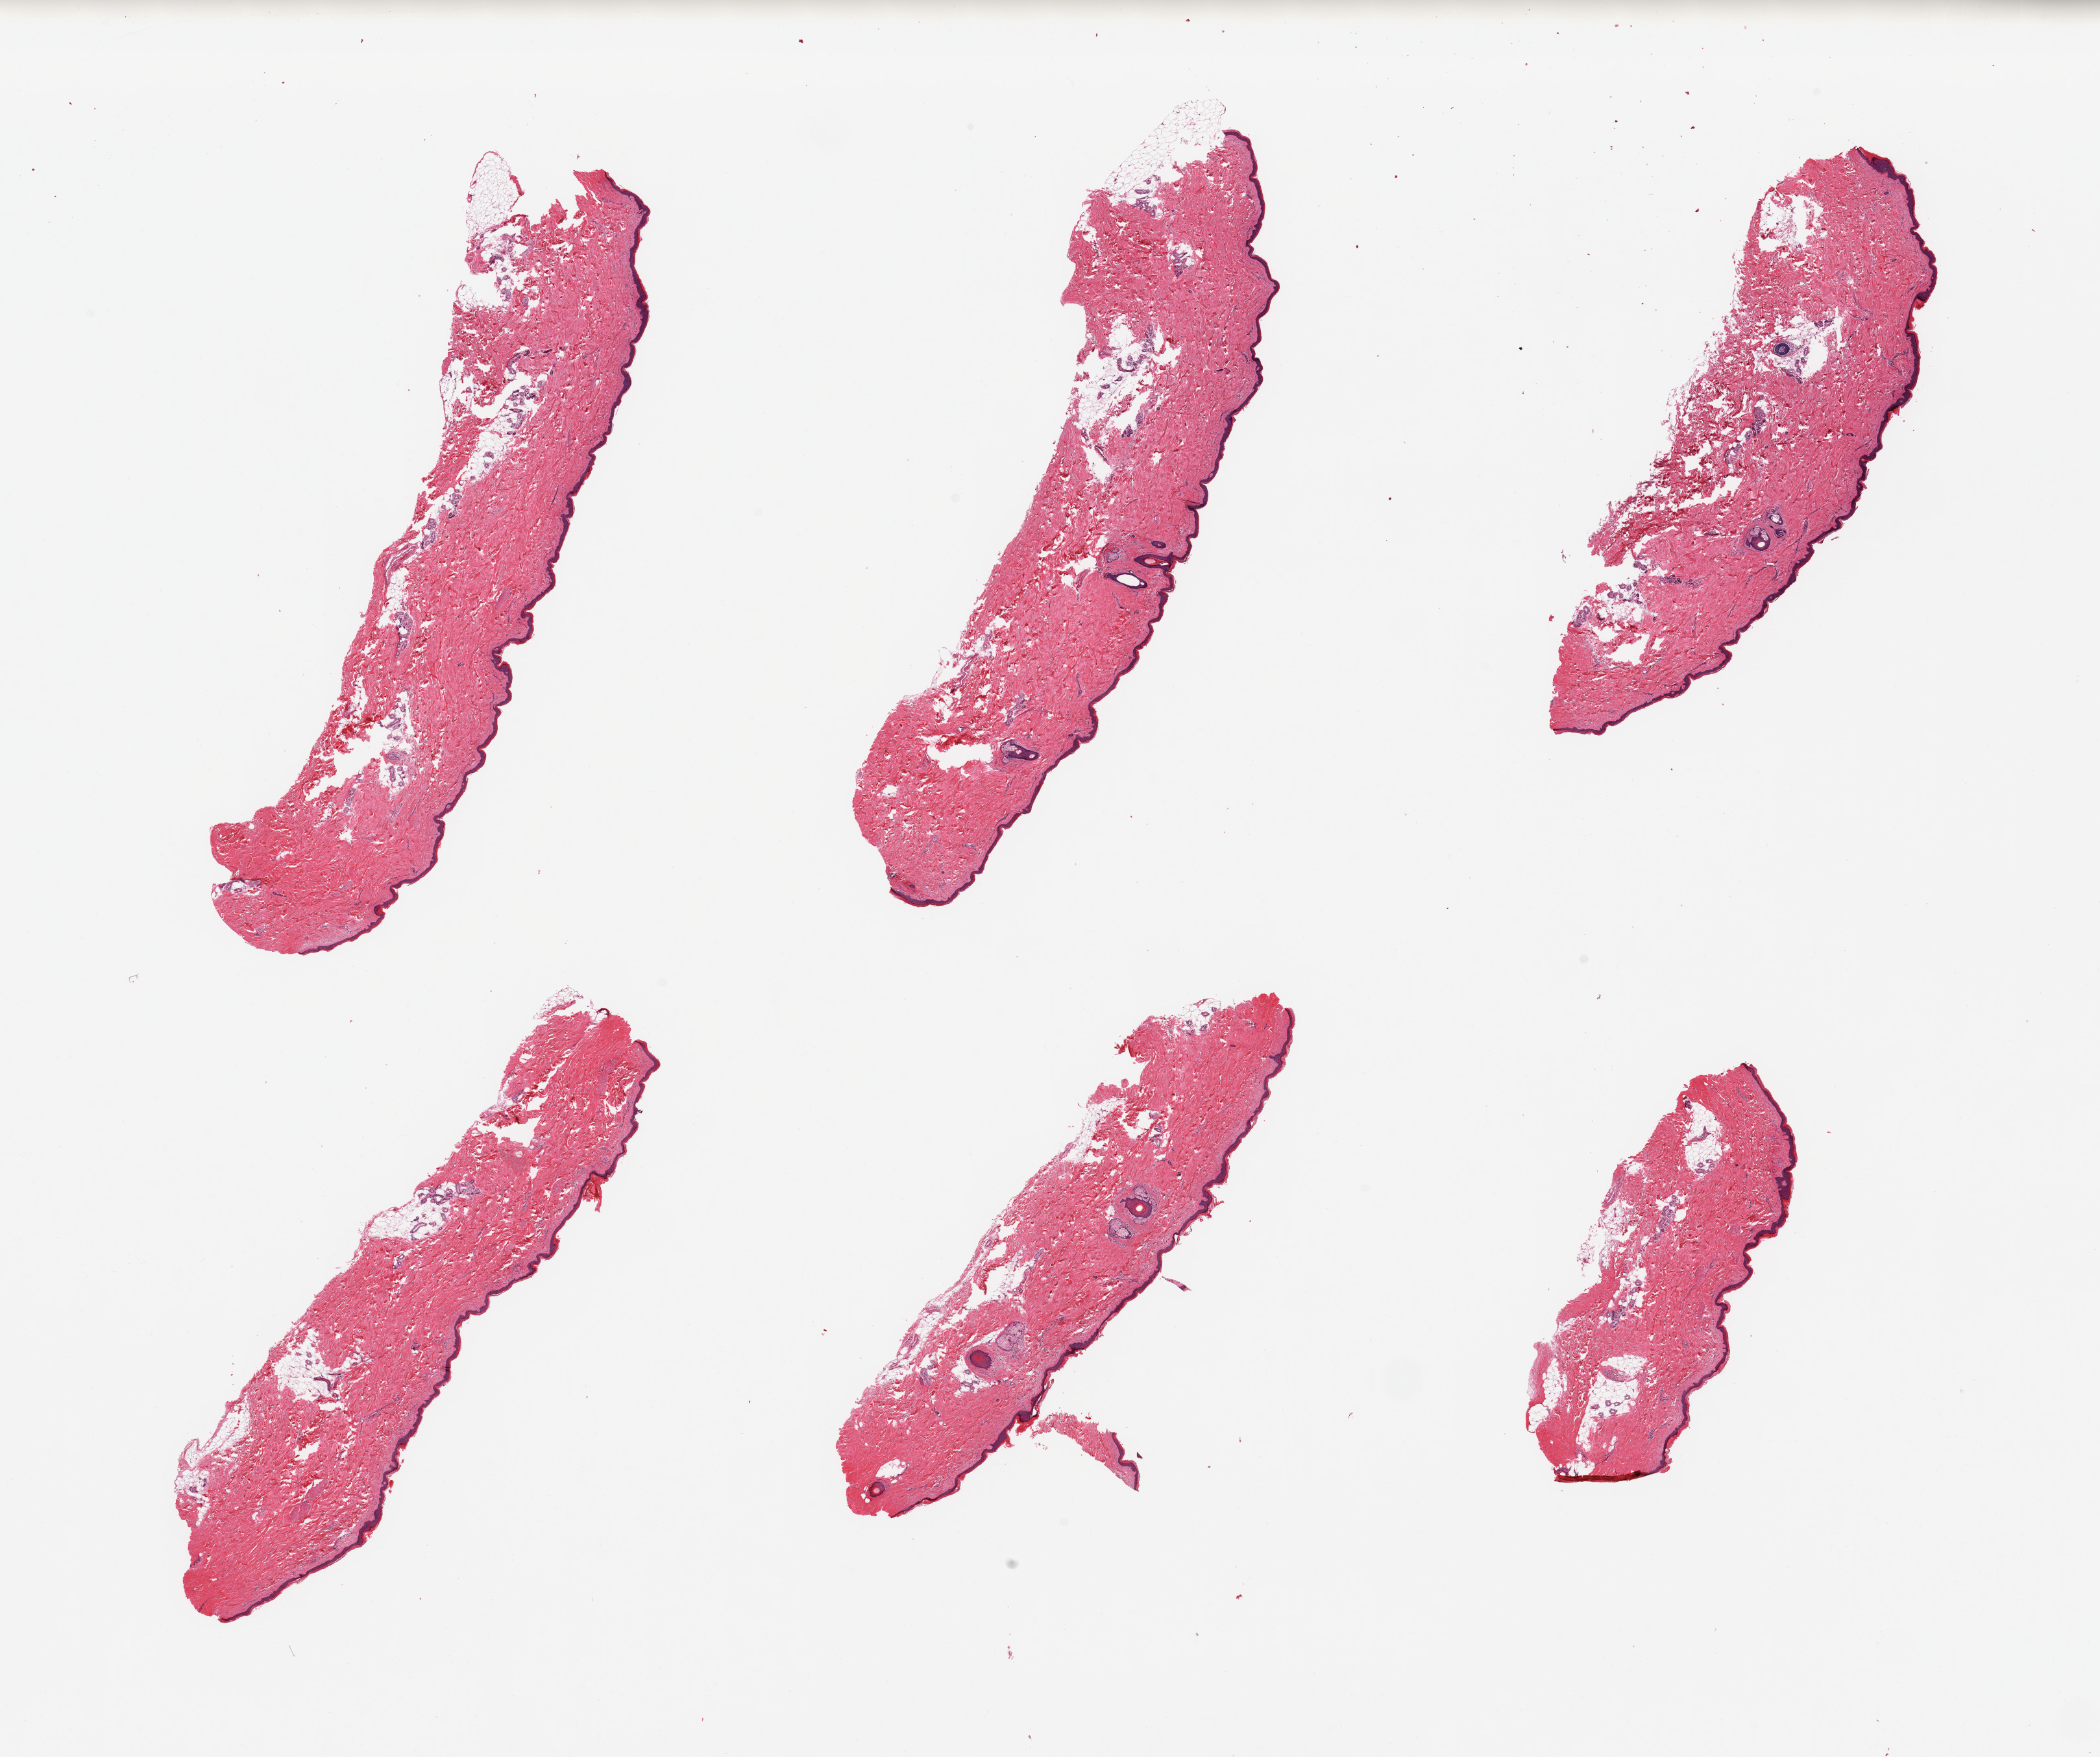
Whole-slide image, hematoxylin and eosin (H&E) stain, brightfield, low-resolution overview of the scanned area, about 25.6 x 21.4 mm (slide scanned at 20x), PAXgene-fixed paraffin-embedded (PFPE) section, section of skin of lower leg (target tissue), tissue donor sample. Donor sex: male.
Review note (as recorded): 6 pieces; well trimmed; 20% dermal fat.